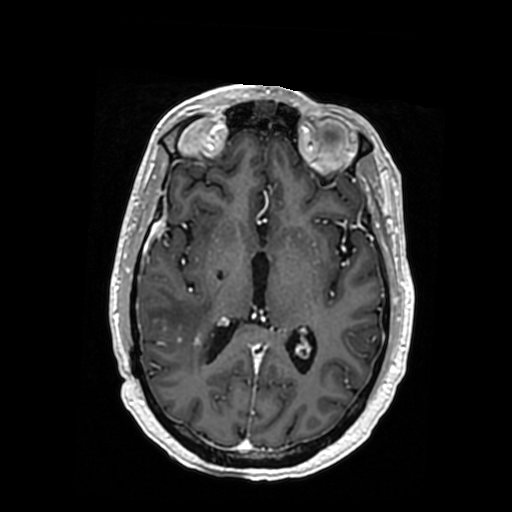
Brain MRI from a brain-tumour surgery series, one axial slice; T1-weighted post-contrast; 0.5 mm slice thickness; 512 × 512 image matrix, field of view 260 × 260 mm. Case-level facts recorded for this patient, not image findings: histopathology: Oligodendroglioma; WHO grade: 3; IDH mutation: yes.
Annotated regions visible in this slice (outlined manually by an expert reader):
- tumour: bounding box [x1, y1, x2, y2] px = [146, 316, 217, 342]